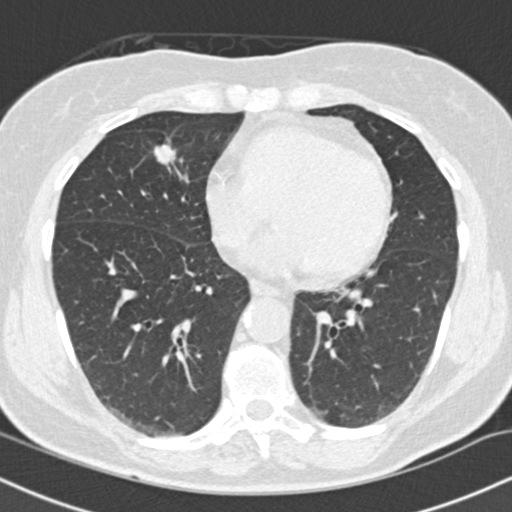
Low-dose screening chest CT, one axial slice; slice 60 of 145 in the series (ordered by position); reconstruction kernel B30f; 120 kVp; lung window (W 1500 / L -600 HU); 2 mm slice thickness; 512 × 512 image matrix.
Outlined on this slice (expert manual segmentation):
- lesion 1 (tumor, middle lobe of right lung): bounding box [x1, y1, x2, y2] px = [153, 139, 176, 166]